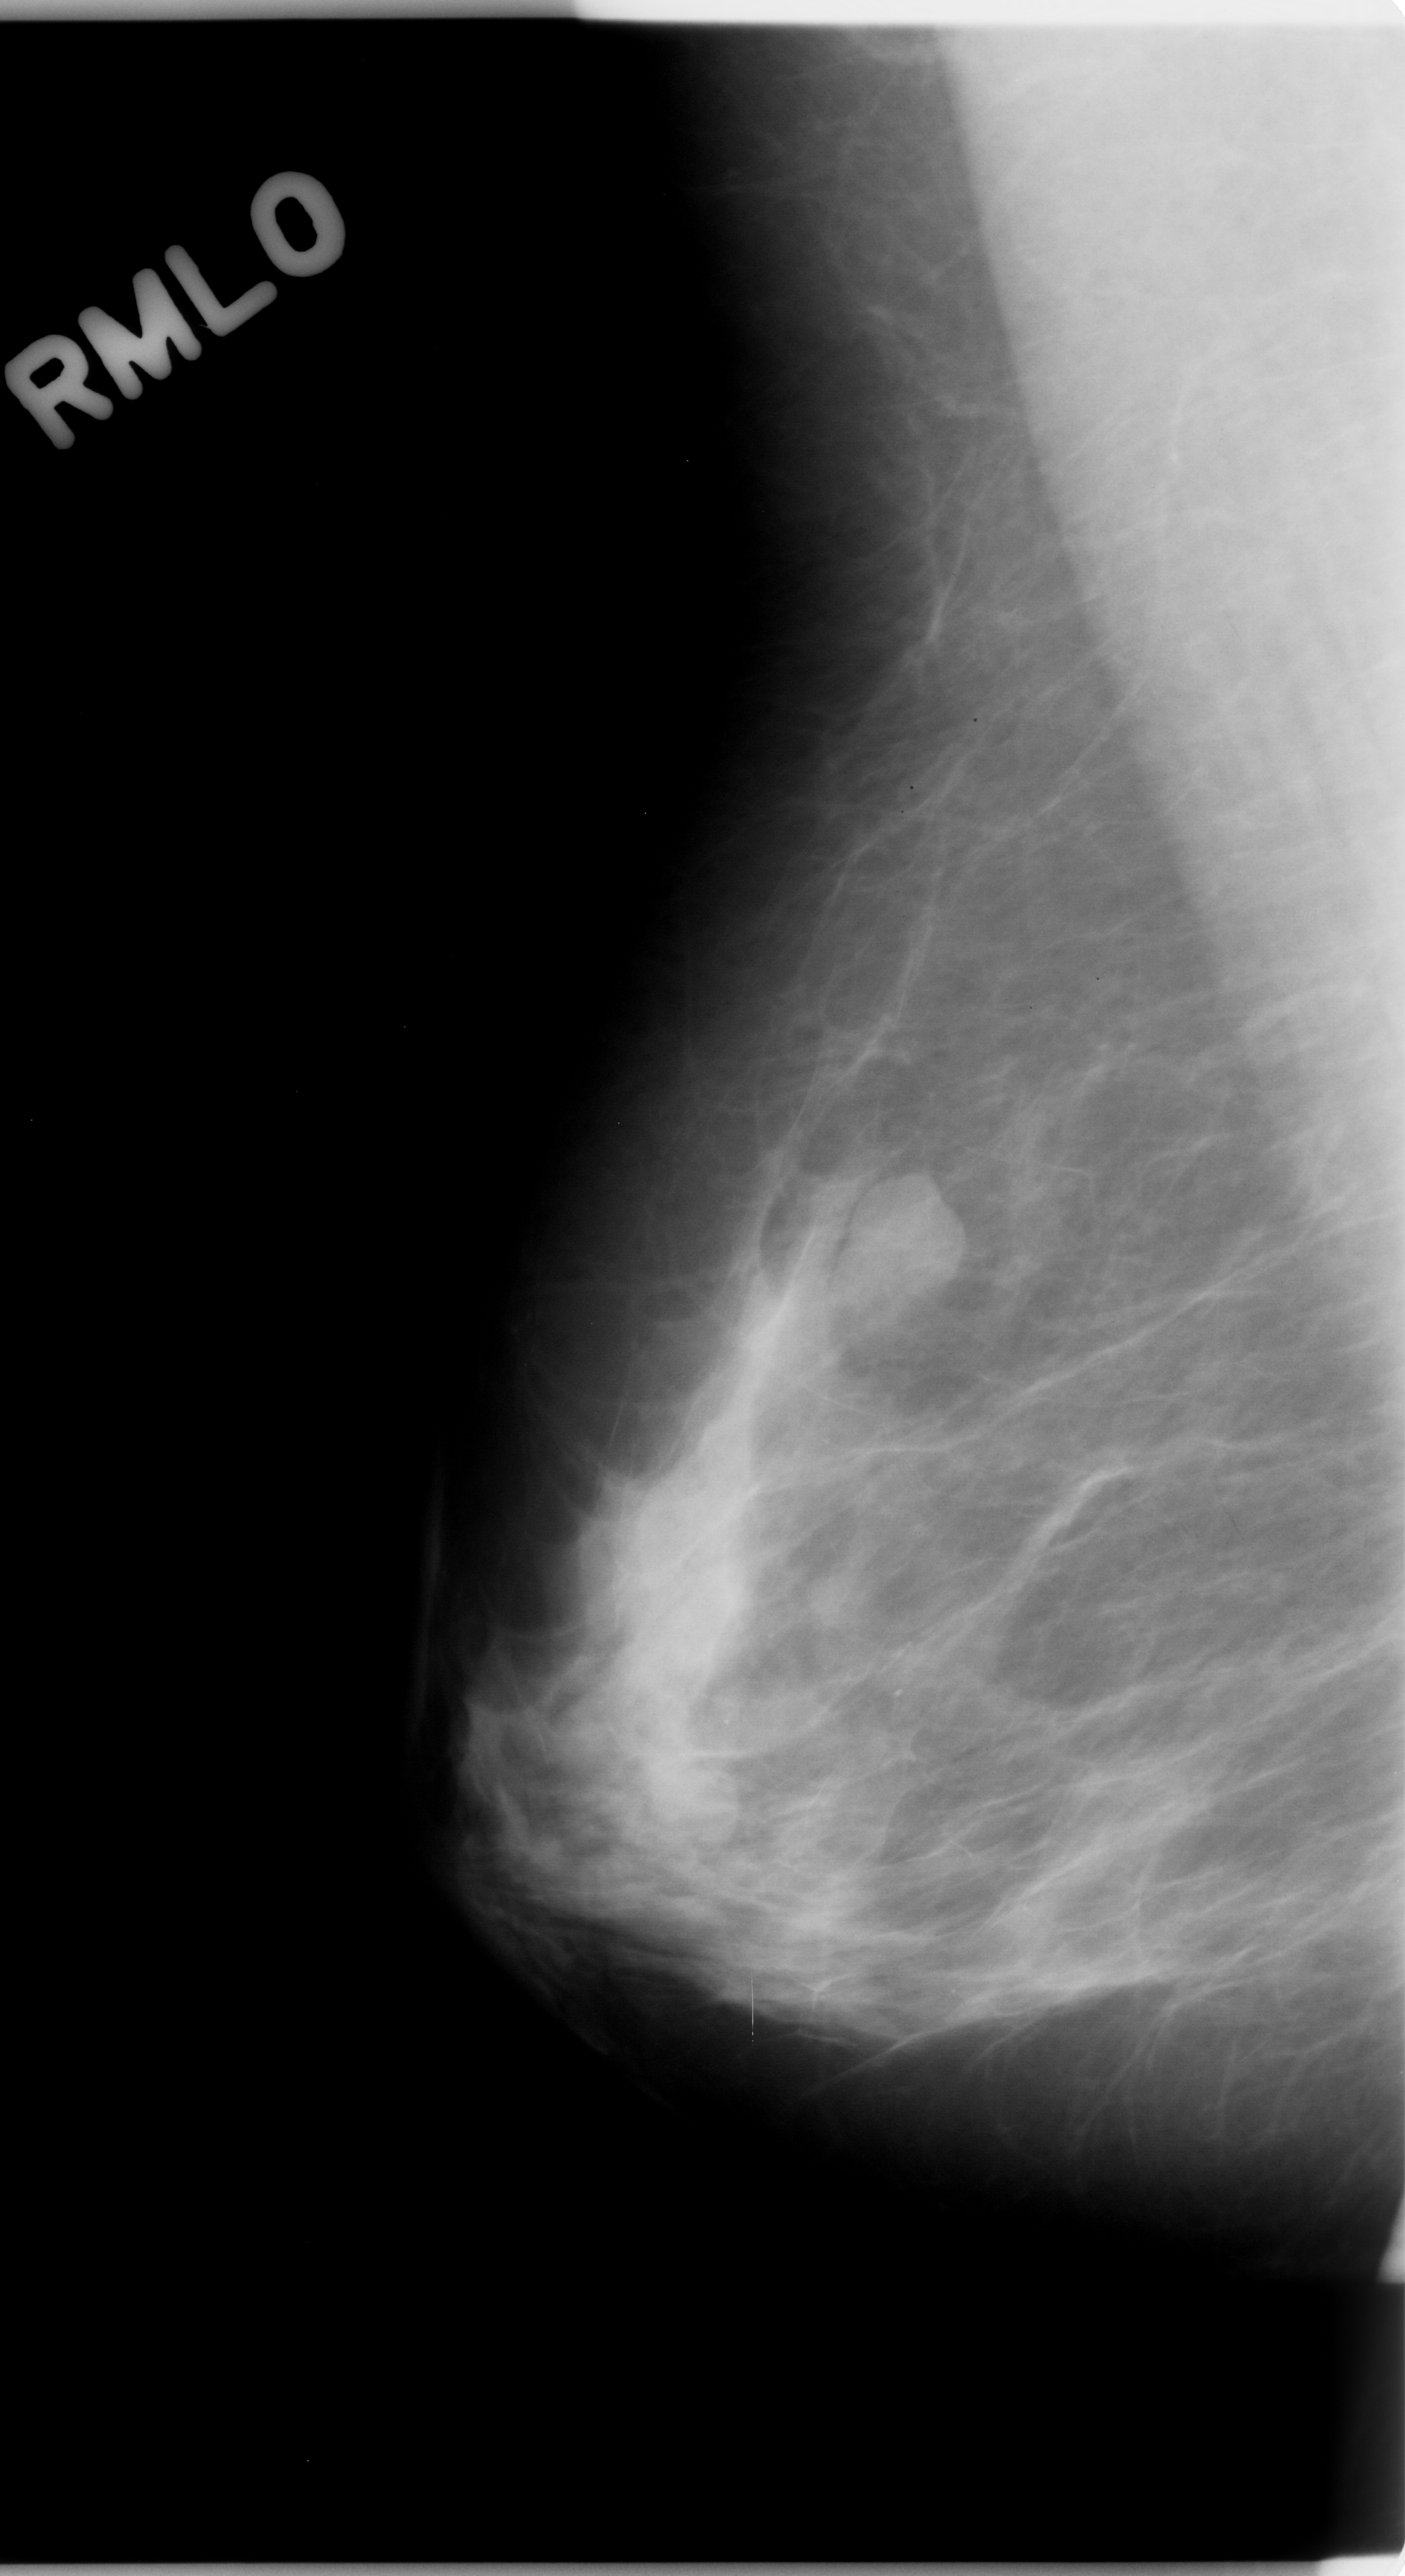
Mammogram (digitized film). Right breast. MLO view. Breast composition: scattered fibroglandular densities (BI-RADS density category 2 of 4). 1405 × 2576 image matrix.
Expert-marked regions of interest on this film, with their recorded descriptors:
- mass, shape oval, margins circumscribed; BI-RADS assessment category 4; pathology (as recorded): benign: bounding box (x1, y1, x2, y2) in pixels: (819, 1188, 958, 1329)